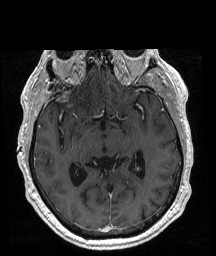
Brain MRI from a brain-tumour surgery series, one axial slice. Position 109 of 192 along the scan axis. T1-weighted post-contrast. 1 mm slice thickness. 216 × 256 image matrix, field of view 211 × 250 mm. From the clinical record (not read from this slice): histopathology: Glioblastoma; WHO grade: 4; IDH mutation: no.
Outlined on this slice (outlined manually by an expert reader):
- tumour: bounding box (x1, y1, x2, y2) in pixels: (40, 87, 59, 100)